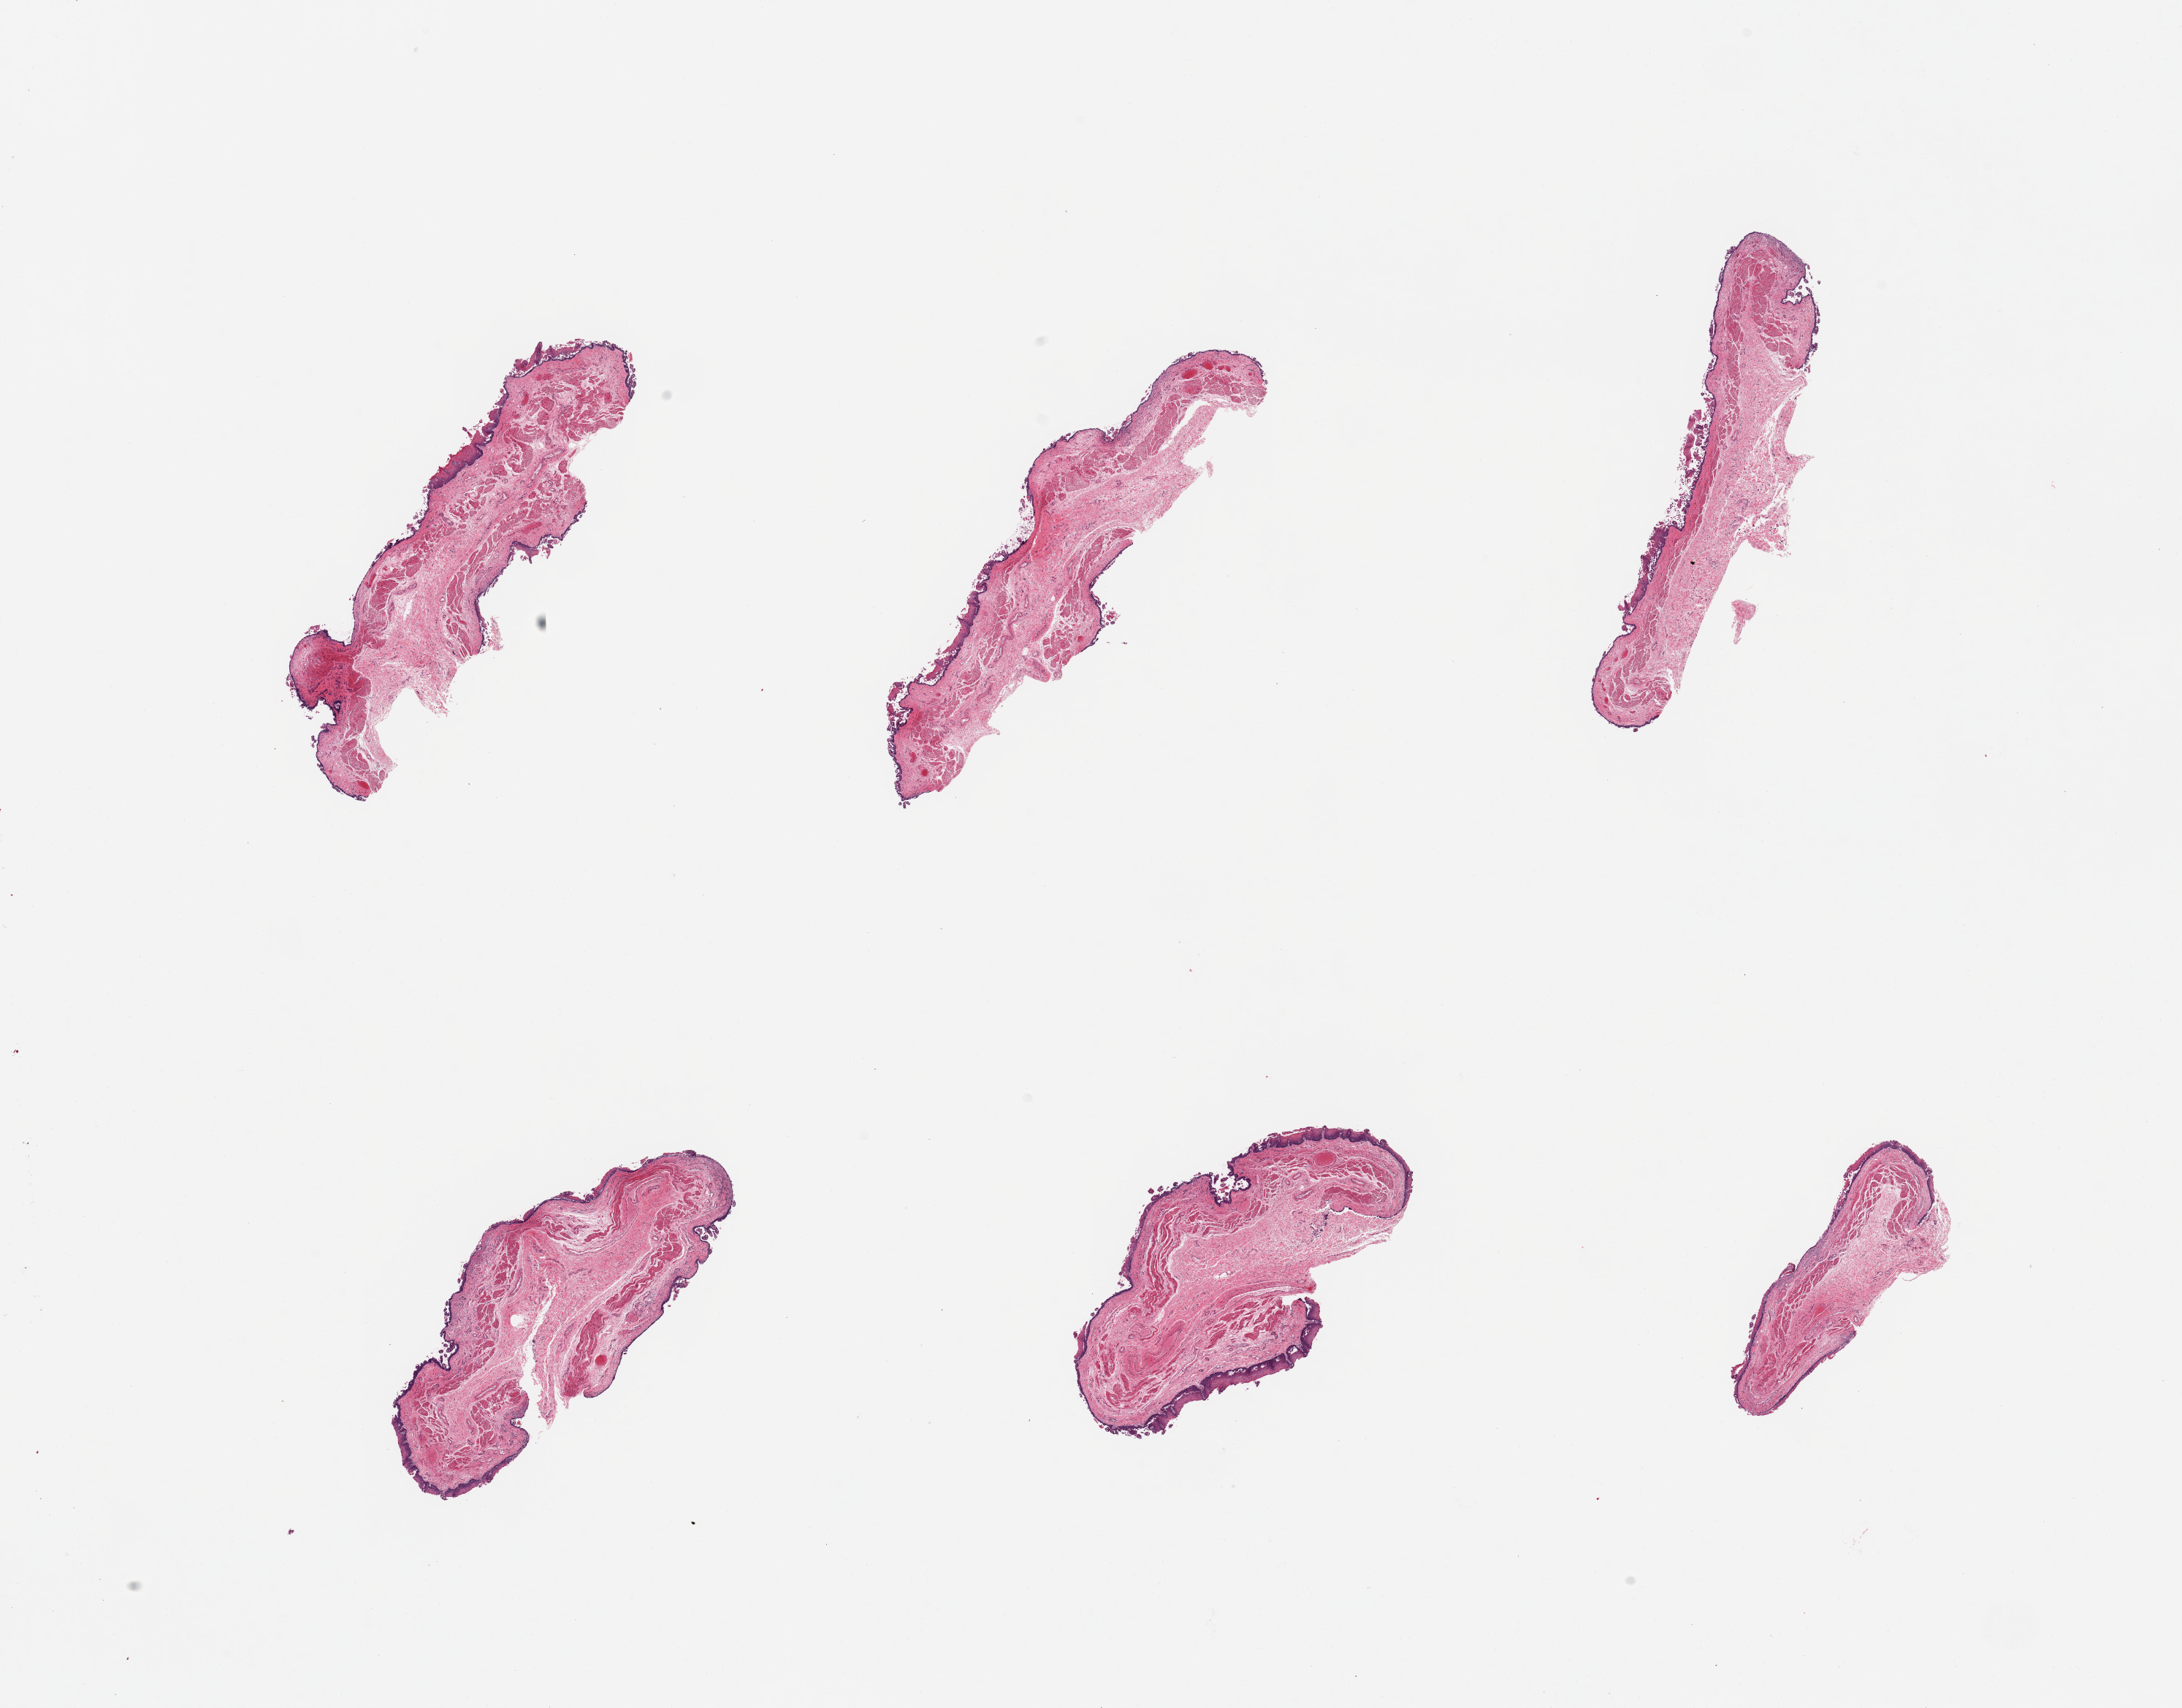
Whole-slide image, H&E stain, shown as a low-resolution overview of the whole scanned area (about 23.6 x 18.5 mm, from a 20x scan). Female donor.
Specimen: PAXgene-fixed paraffin-embedded (PFPE) section; target tissue: esophageal mucous membrane; tissue donor sample.